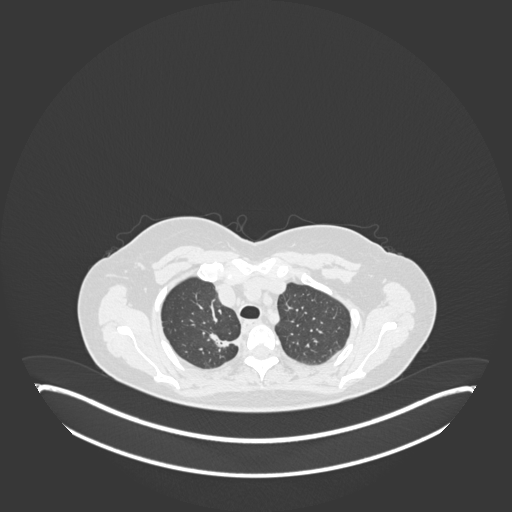
Chest CT, one axial slice. Slice 144 of 181 in the series (ordered by position). Lung window (W 1500 / L -600 HU). 512 × 512 image matrix. Patient: female, 65 years. Case-level facts recorded for this patient, not image findings: clinical TNM (as recorded): T1b N0 M0; histopathological grade: G2.
Annotated regions visible in this slice (bounding box drawn by a radiologist):
- lung tumour (recorded histology: adenocarcinoma): box from (x=201, y=325) to (x=243, y=353) px